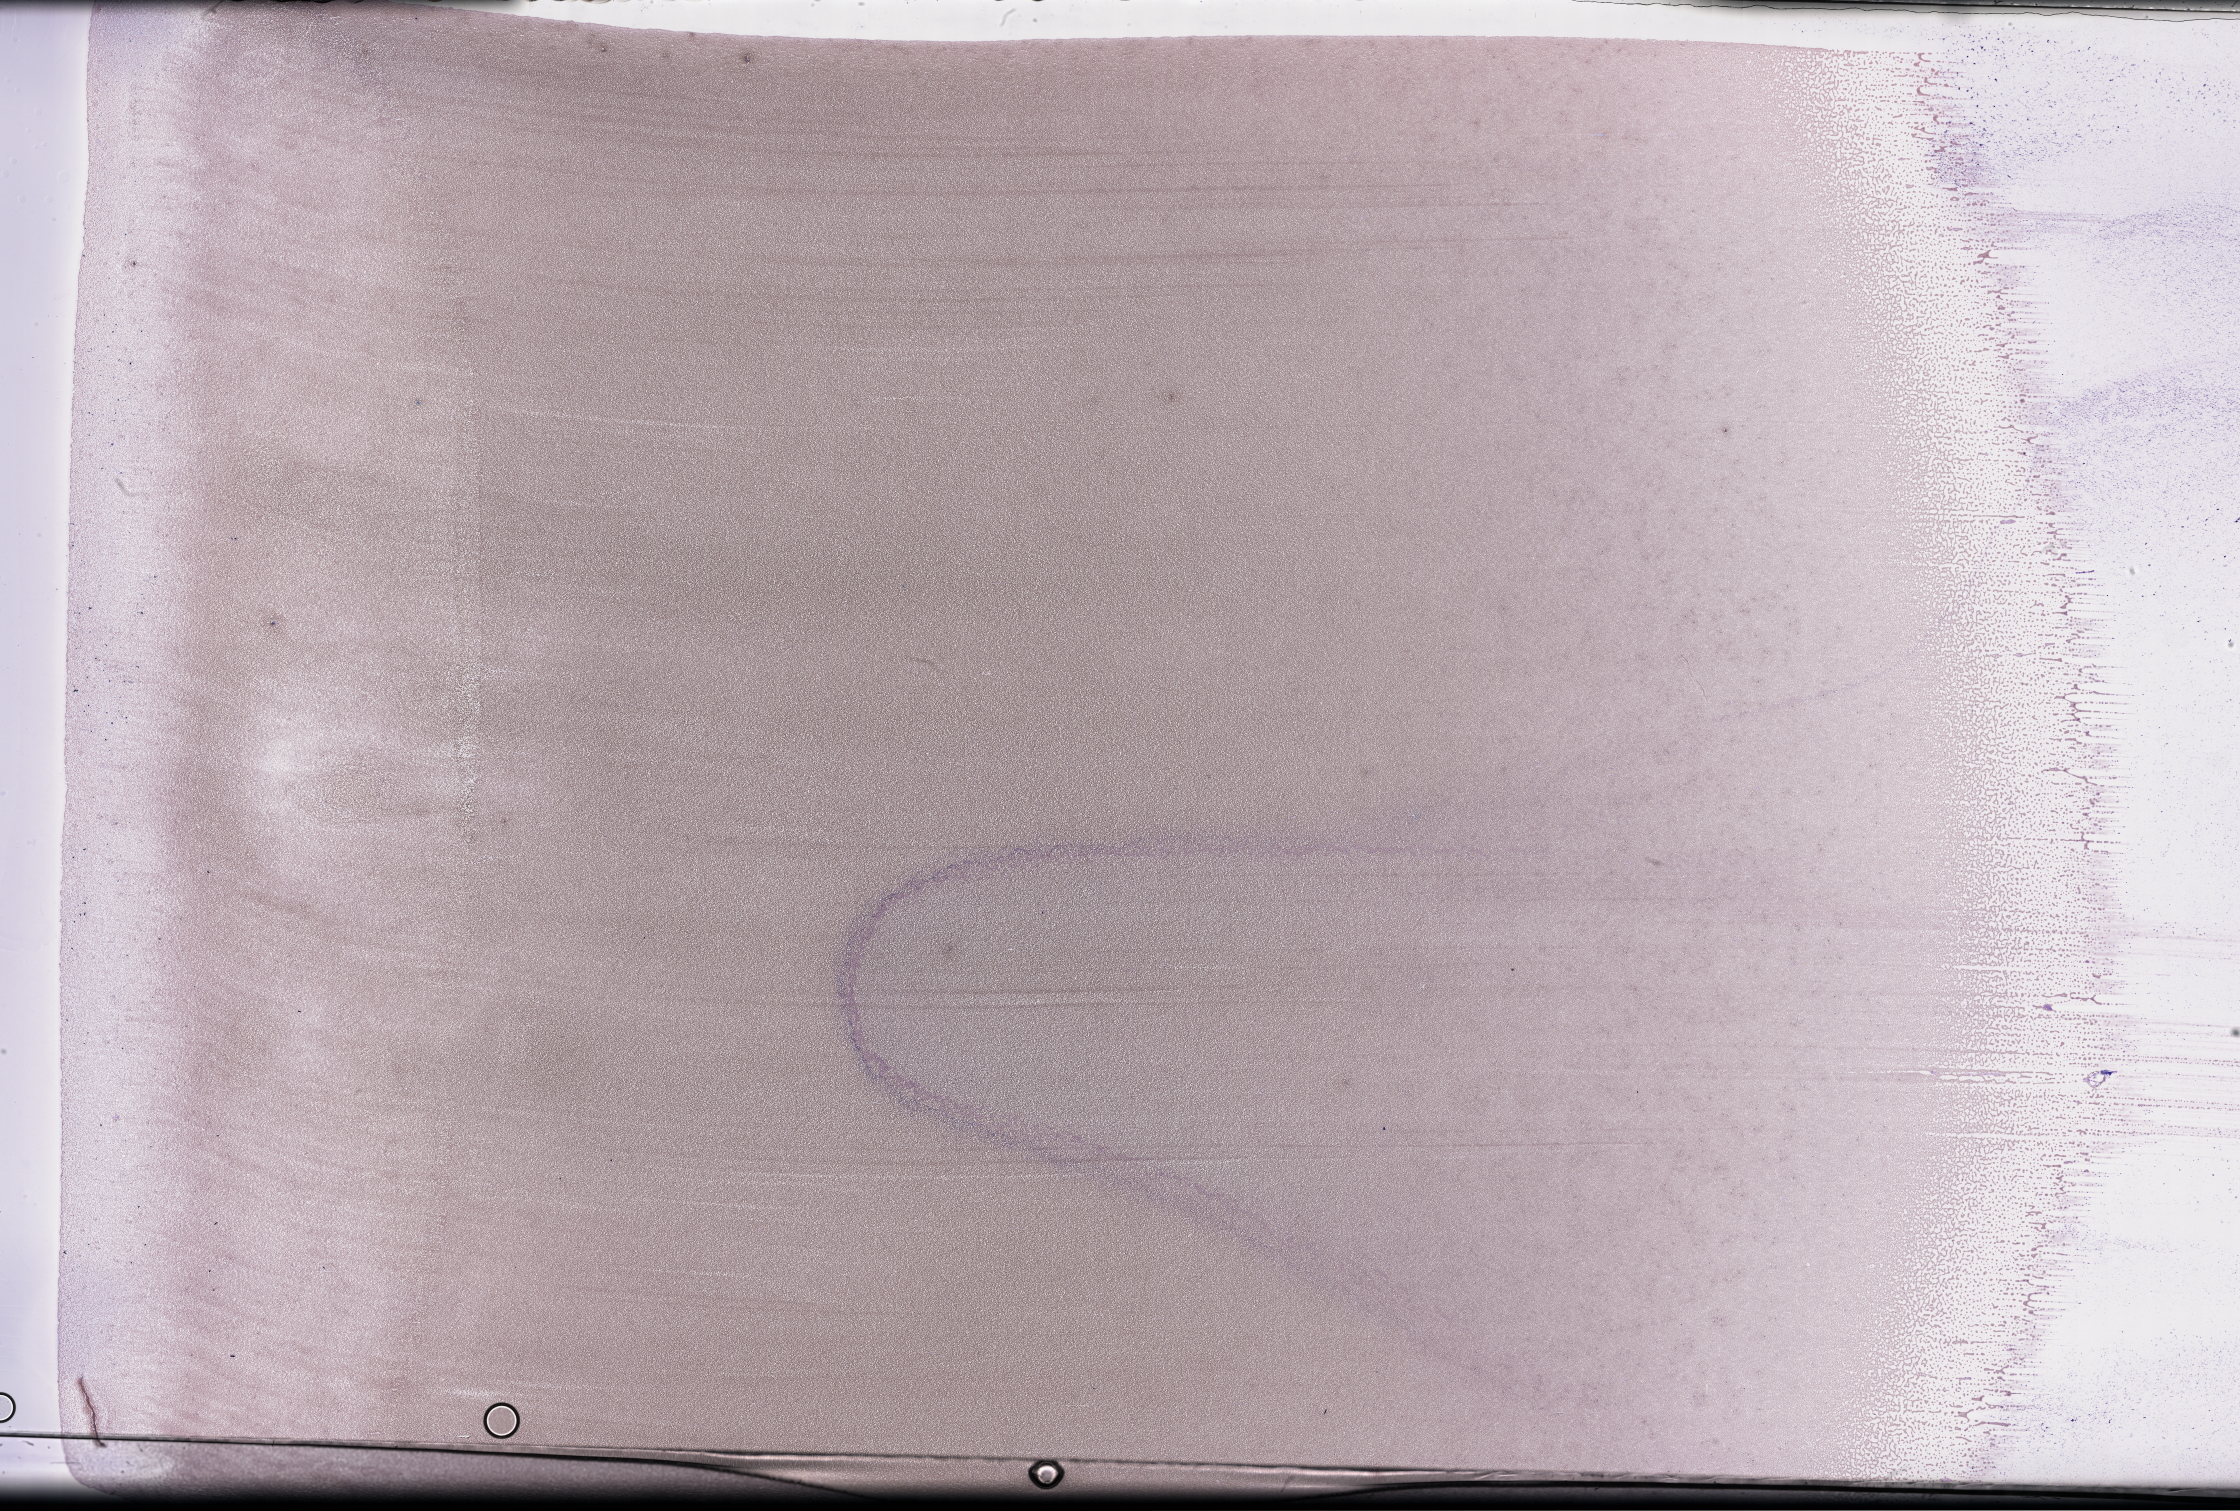
Whole-slide image of a whole blood smear, Wright–Giemsa stain, whole scanned area (about 36.2 x 24.4 mm) shown as a low-resolution overview. Male patient.
Patient diagnosis: Plasma Cell Myeloma.